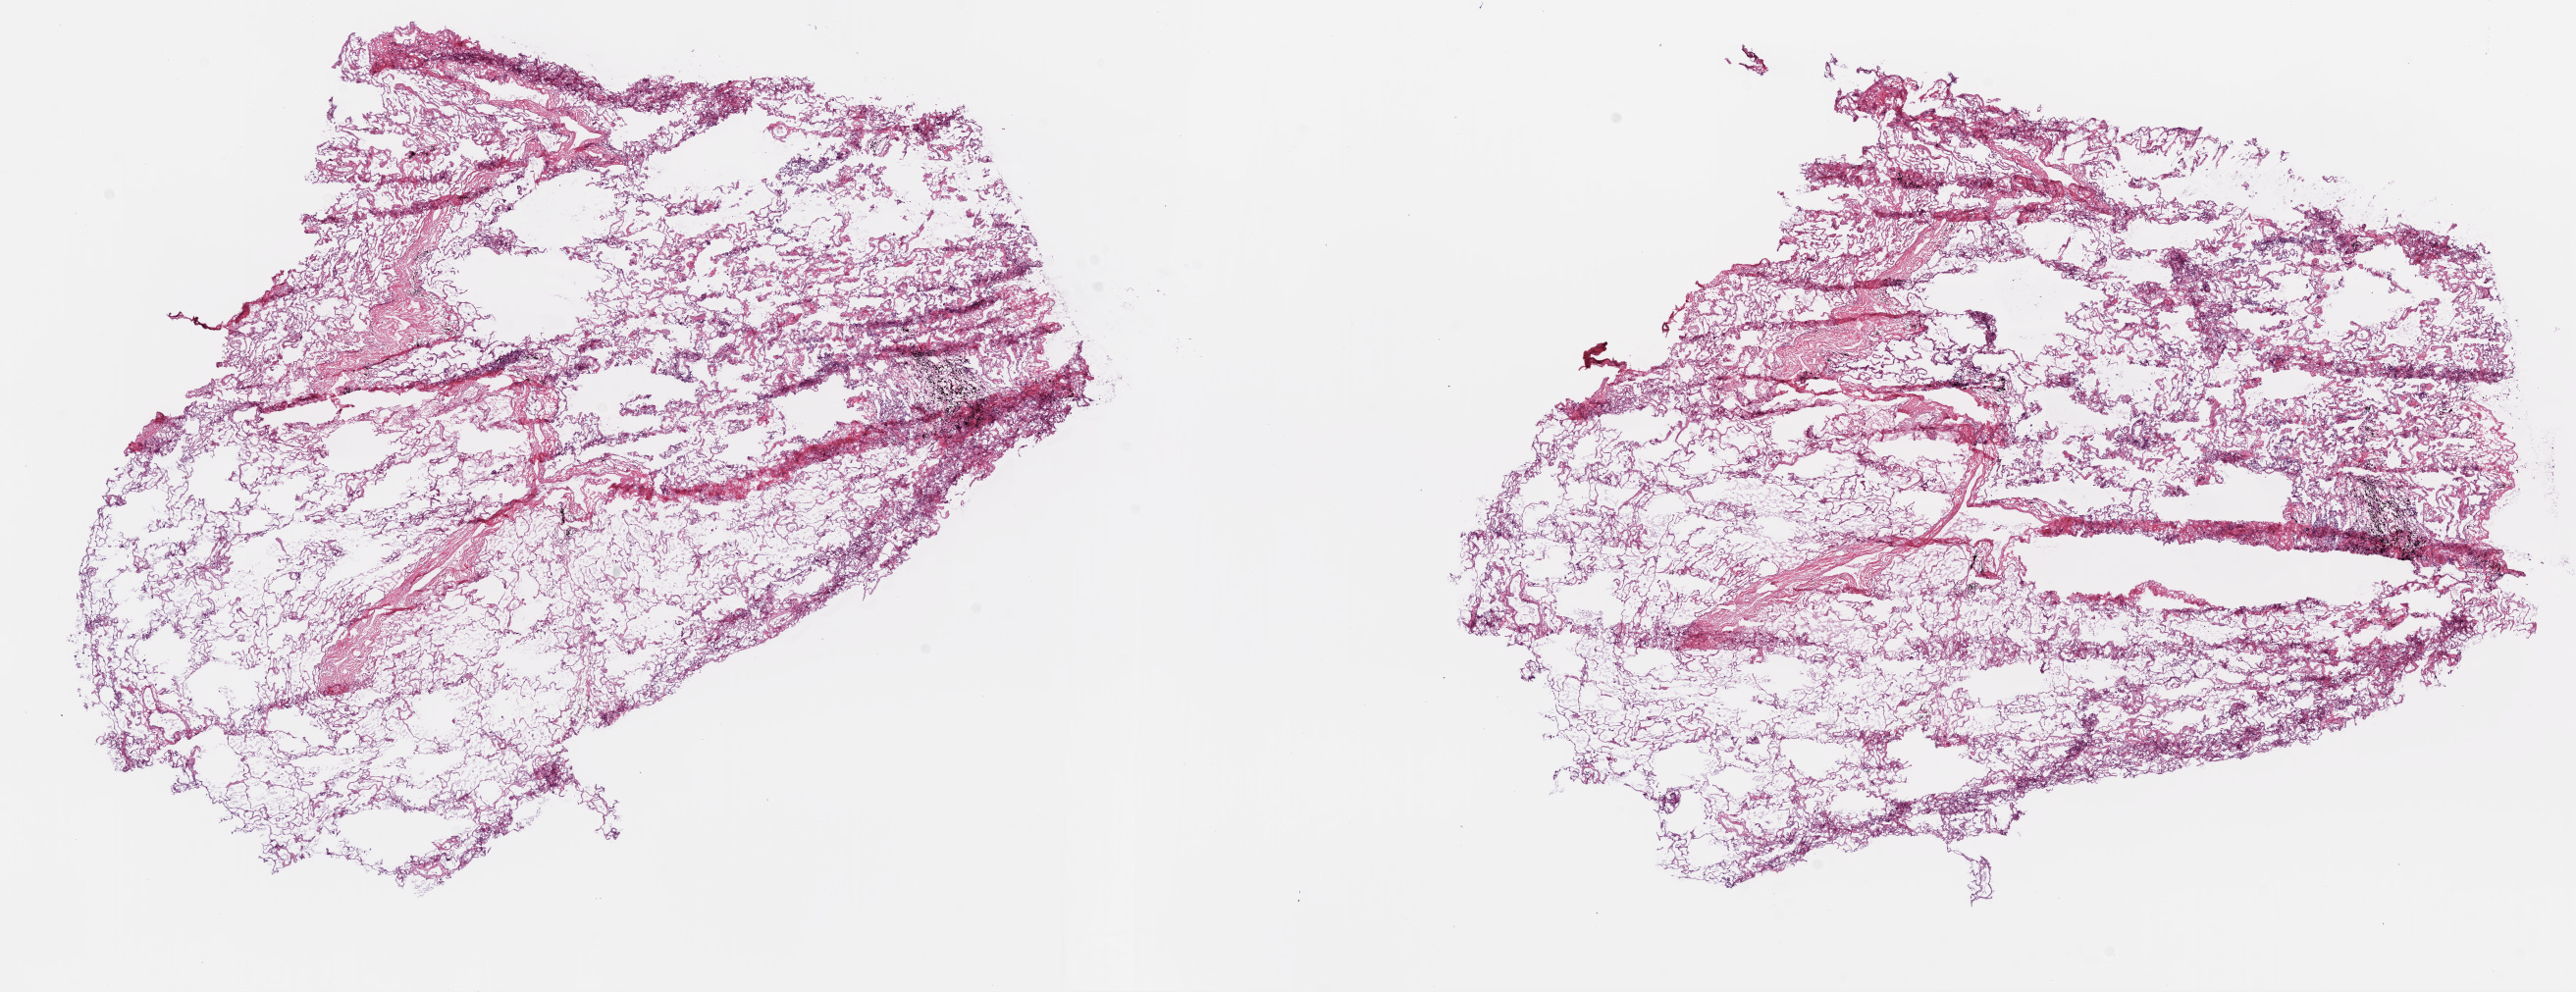
Whole-slide histology image, H&E — whole scanned area (about 21.1 x 8.1 mm, acquisition: 20x scan) shown as a low-resolution overview. Frozen section from the bottom of the tissue portion. Solid tissue normal (non-tumour tissue) sample from the lung. Female, age 83 years at initial diagnosis.
This section: solid tissue normal (non-tumour) sample from the same patient. Patient diagnosis: Squamous cell carcinoma, NOS.